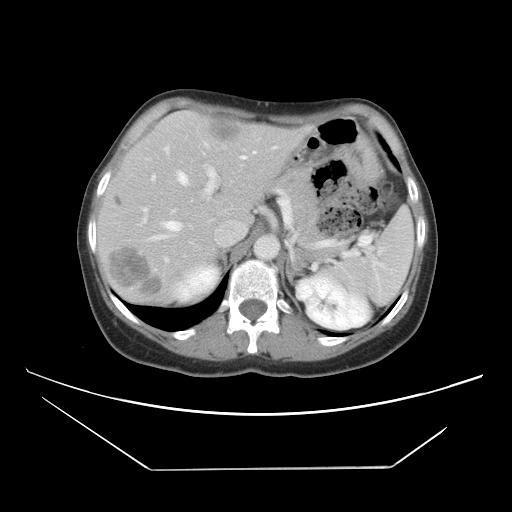
Contrast-enhanced abdominal CT, one axial slice; intravenous contrast given; soft-tissue window (W 400 / L 40 HU); 5 mm slice thickness; 512 × 512 image matrix, field of view 399 × 399 mm. Female patient, age 52 years. From the clinical record (not read from this slice): diagnosis: colorectal cancer liver metastases, imaged before liver resection; multiple liver metastases: yes; largest metastasis: 5.5 cm; disease in both lobes: yes.
Outlined on this slice (expert manual segmentation):
- hepatic veins: bounding box (x1, y1, x2, y2) in pixels: (139, 147, 277, 241)
- liver: (99, 112, 305, 302)
- planned liver remnant (the part of the liver to remain after resection): (117, 117, 239, 226)
- portal vein (with intrahepatic branches): (142, 146, 292, 224)
- liver metastasis: (213, 122, 242, 139)
- liver metastasis: (115, 197, 123, 206)
- liver metastasis: (111, 248, 162, 295)